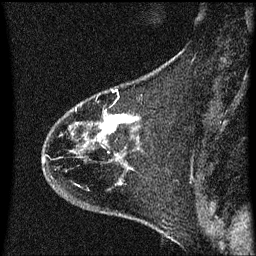
Breast MRI (dynamic contrast-enhanced), one sagittal slice. Dynamic contrast-enhanced series, image 2 of 3 at this slice position (ordered by acquisition). 1.5 T. TE 4.2 ms, TR 8.4 ms. 2 mm slice thickness. 256 × 256 image matrix, field of view 200 × 200 mm. Female patient, age 35 years. From the clinical record (not read from this slice): setting: breast cancer imaged before/during neoadjuvant chemotherapy; receptor status: HER2-positive.
Annotated regions visible in this slice (semi-automatic segmentation, software-assisted and operator-edited):
- analysis volume of interest (the breast-tissue region the enhancement analysis was run in; not a lesion): bounding box [x1, y1, x2, y2] px = [42, 68, 174, 173]
- tumour enhancement mask (voxels above the 70 % enhancement threshold inside the analysis volume of interest): [106, 116, 128, 133]